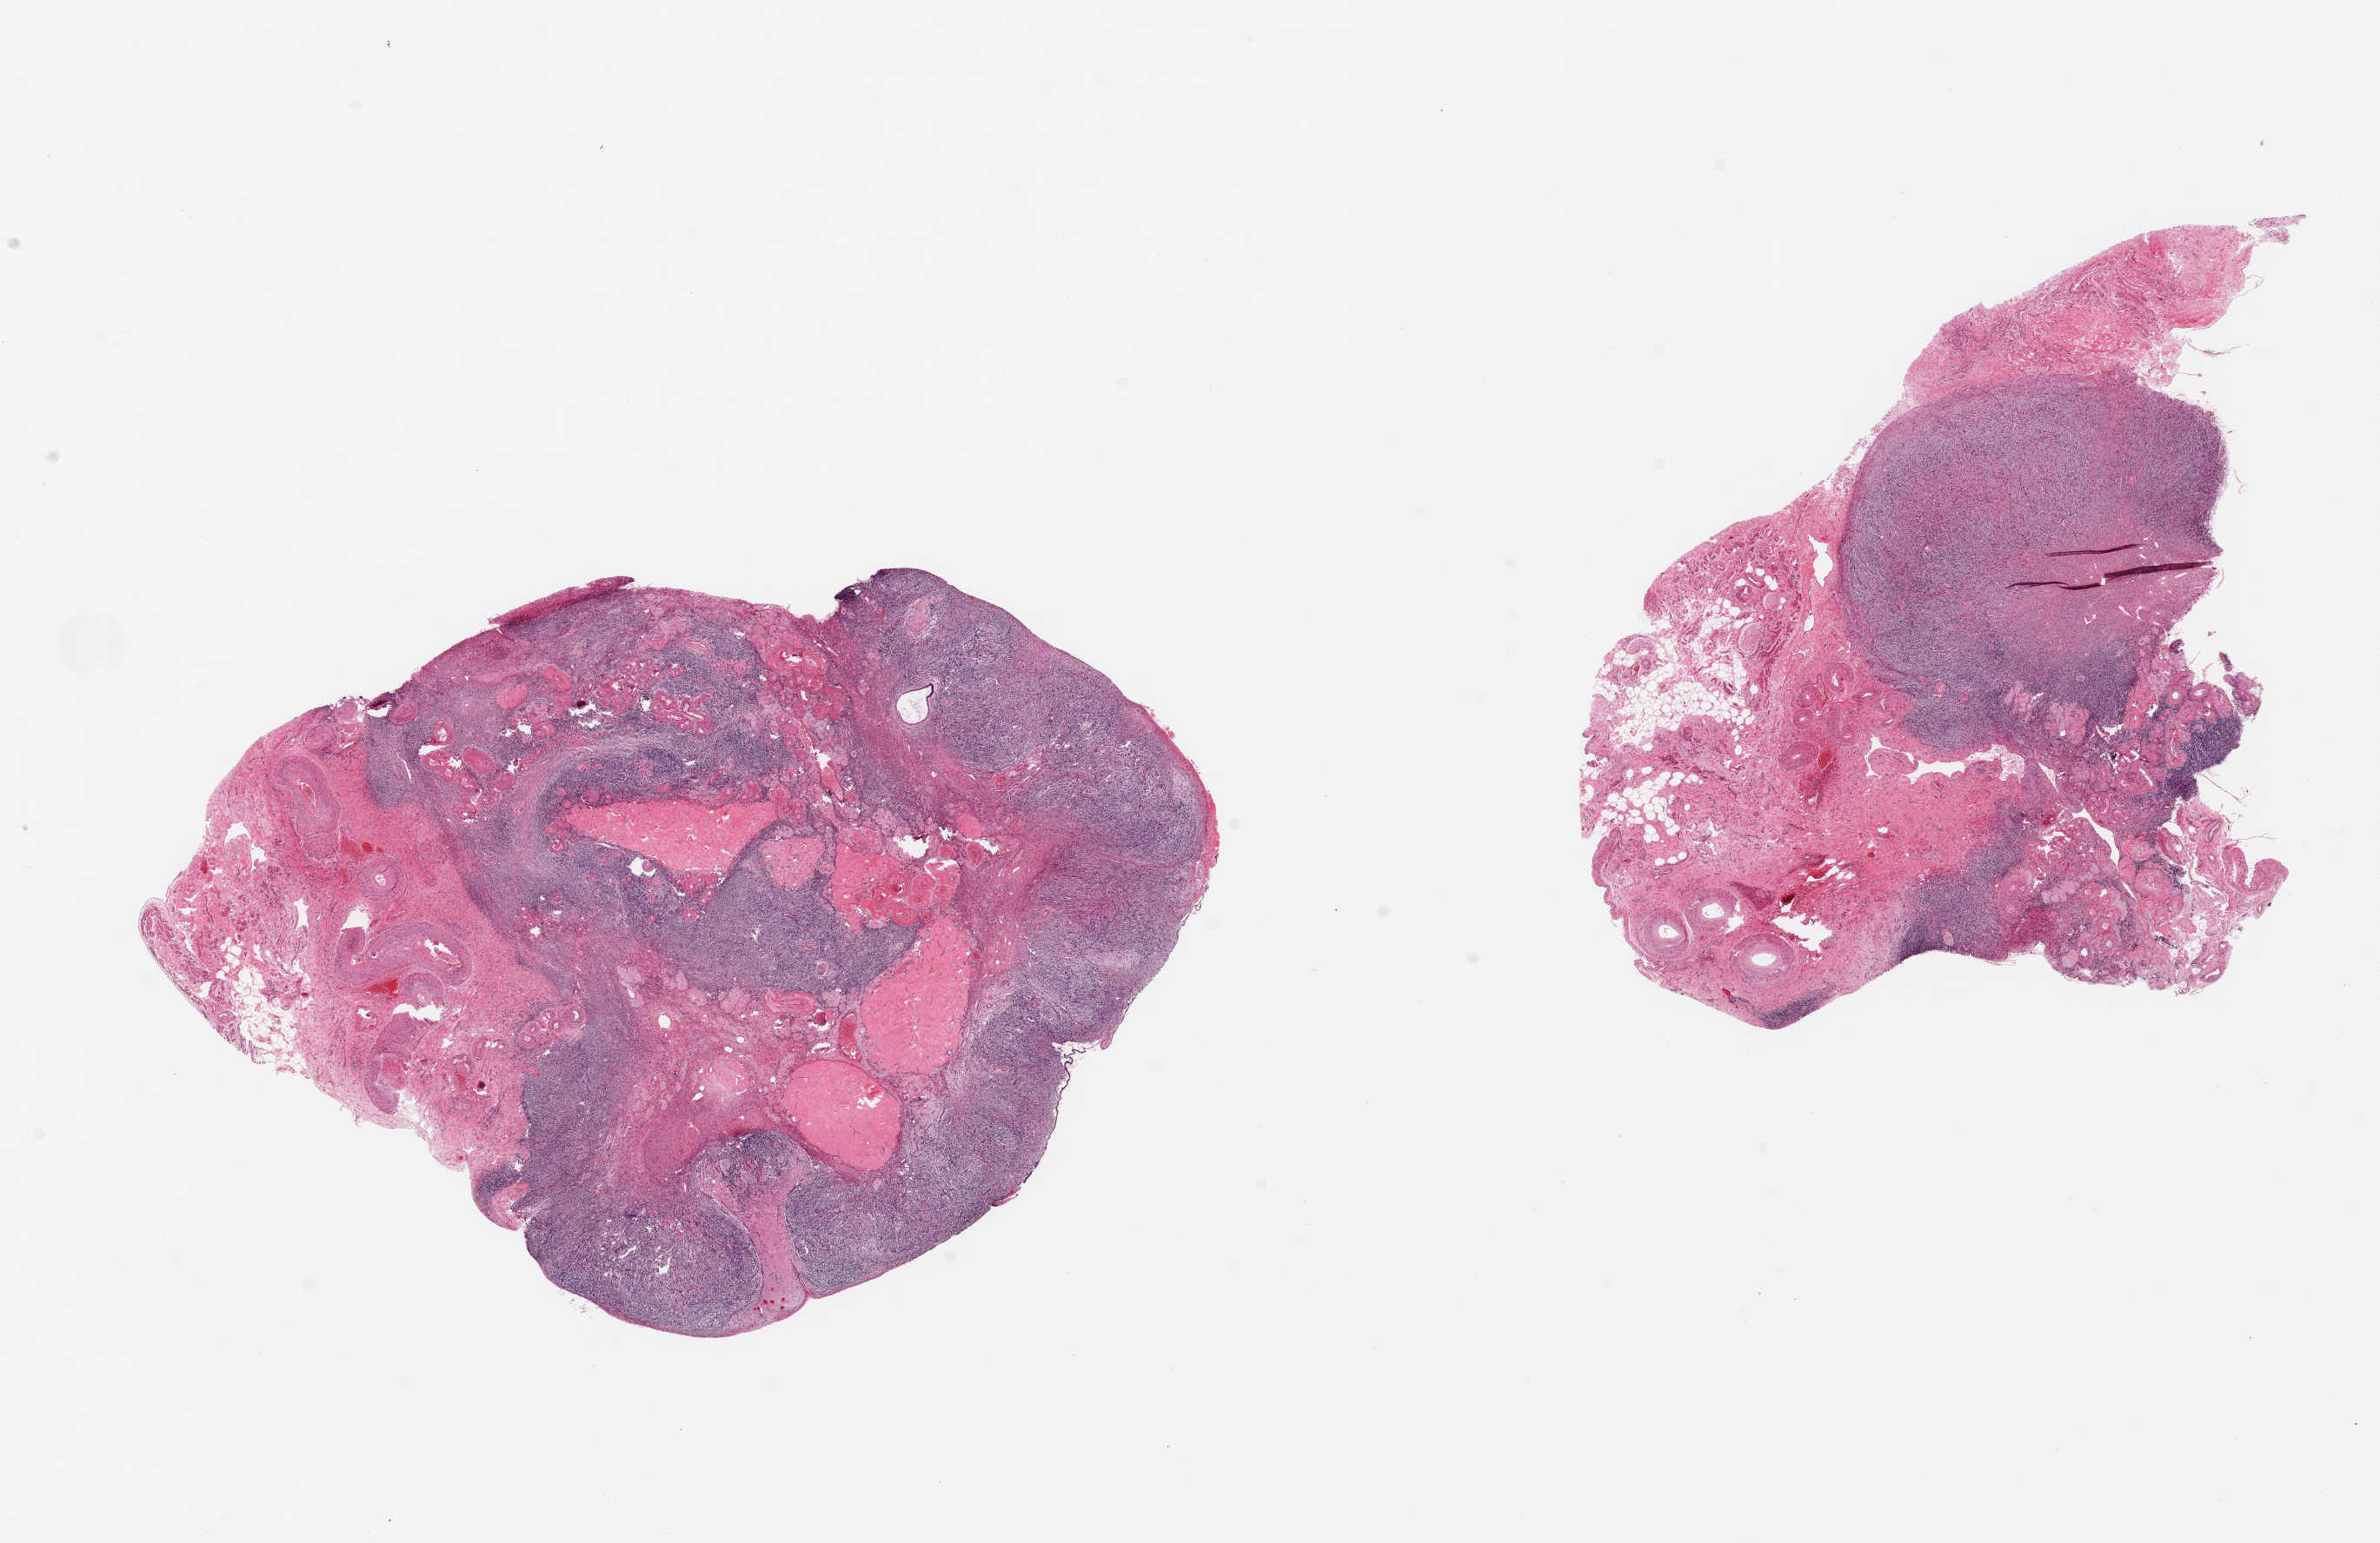
Digitized hematoxylin and eosin (H&E)-stained section — shown as a low-resolution overview of the whole scanned area (about 21.7 x 14.0 mm); PAXgene-fixed paraffin-embedded (PFPE) section; target tissue: ovary; donor tissue sample. Donor sex: female.
Reviewer comment on this tissue sample: 2 pieces, 7.5x7 & 7x7mm; atrophic with corpora albicans; 20-40% fibrovascular and adipose tissue.